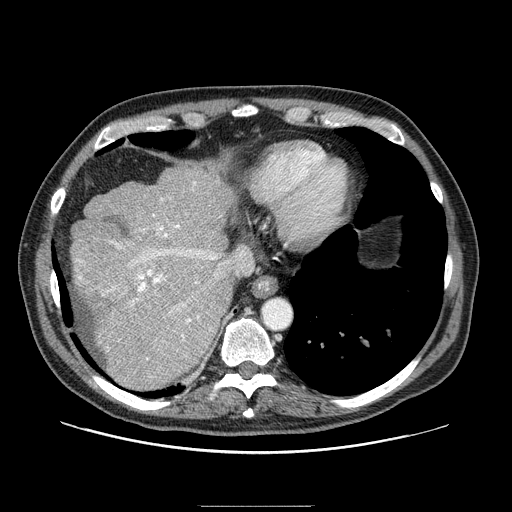
Contrast-enhanced abdominal CT (liver protocol), one axial slice; slice 72 of 99 in the series (ordered by position); reconstruction kernel STANDARD; one of 2 acquisitions stored at this slice position; soft-tissue window (W 400 / L 40 HU); 2.5 mm slice thickness; 512 × 512 image matrix, field of view 400 × 400 mm. Case-level facts recorded for this patient, not image findings: diagnosis: hepatocellular carcinoma (patient treated with transarterial chemoembolisation; whether this scan precedes or follows treatment is not stated here); TNM stage (as recorded): Stage-II; Child-Pugh class: A; tumour nodularity: multinodular.
Annotated regions visible in this slice (semi-automatically segmented with operator editing):
- abdominal aorta: box from (x=262, y=298) to (x=291, y=328) px
- liver parenchyma outside the tumour (the mass and vessels are separate outlines, so this box may not span the whole liver): (x=70, y=164)–(x=234, y=388)
- liver vessels: (x=77, y=181)–(x=221, y=360)